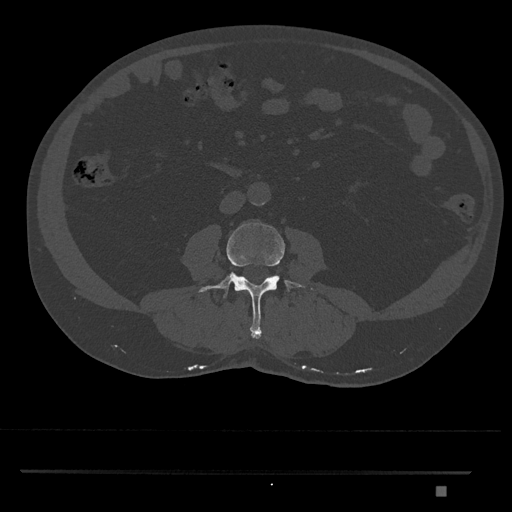
CT including the spine, one axial slice. Slice 677 of 1134 in the series (ordered by position). Reconstruction kernel Br40s/3. Bone window (W 1800 / L 400 HU). 512 × 512 image matrix, field of view 429 × 429 mm. Patient: male, 65 years. Case-level facts recorded for this patient, not image findings: primary cancer: prostate.
Annotated regions visible in this slice (semi-automatic segmentation, software-assisted and operator-edited):
- L3 vertebra: bounding box (x1, y1, x2, y2) in pixels: (198, 222, 315, 339)